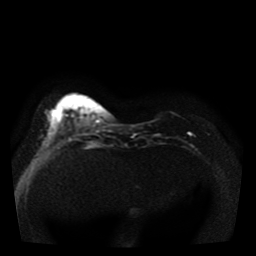
Breast MRI, one axial slice; slice 11 of 41 in the series (ordered by position); diffusion-weighted series; image 2 of 4 stored at this slice position (different b-values; order by instance number); 1.5 T; 256 × 256 image matrix, field of view 330 × 330 mm. Female patient.
Outlined on this slice (manually delineated by an expert):
- tumour on diffusion-weighted imaging: box from (x=188, y=133) to (x=192, y=135) px